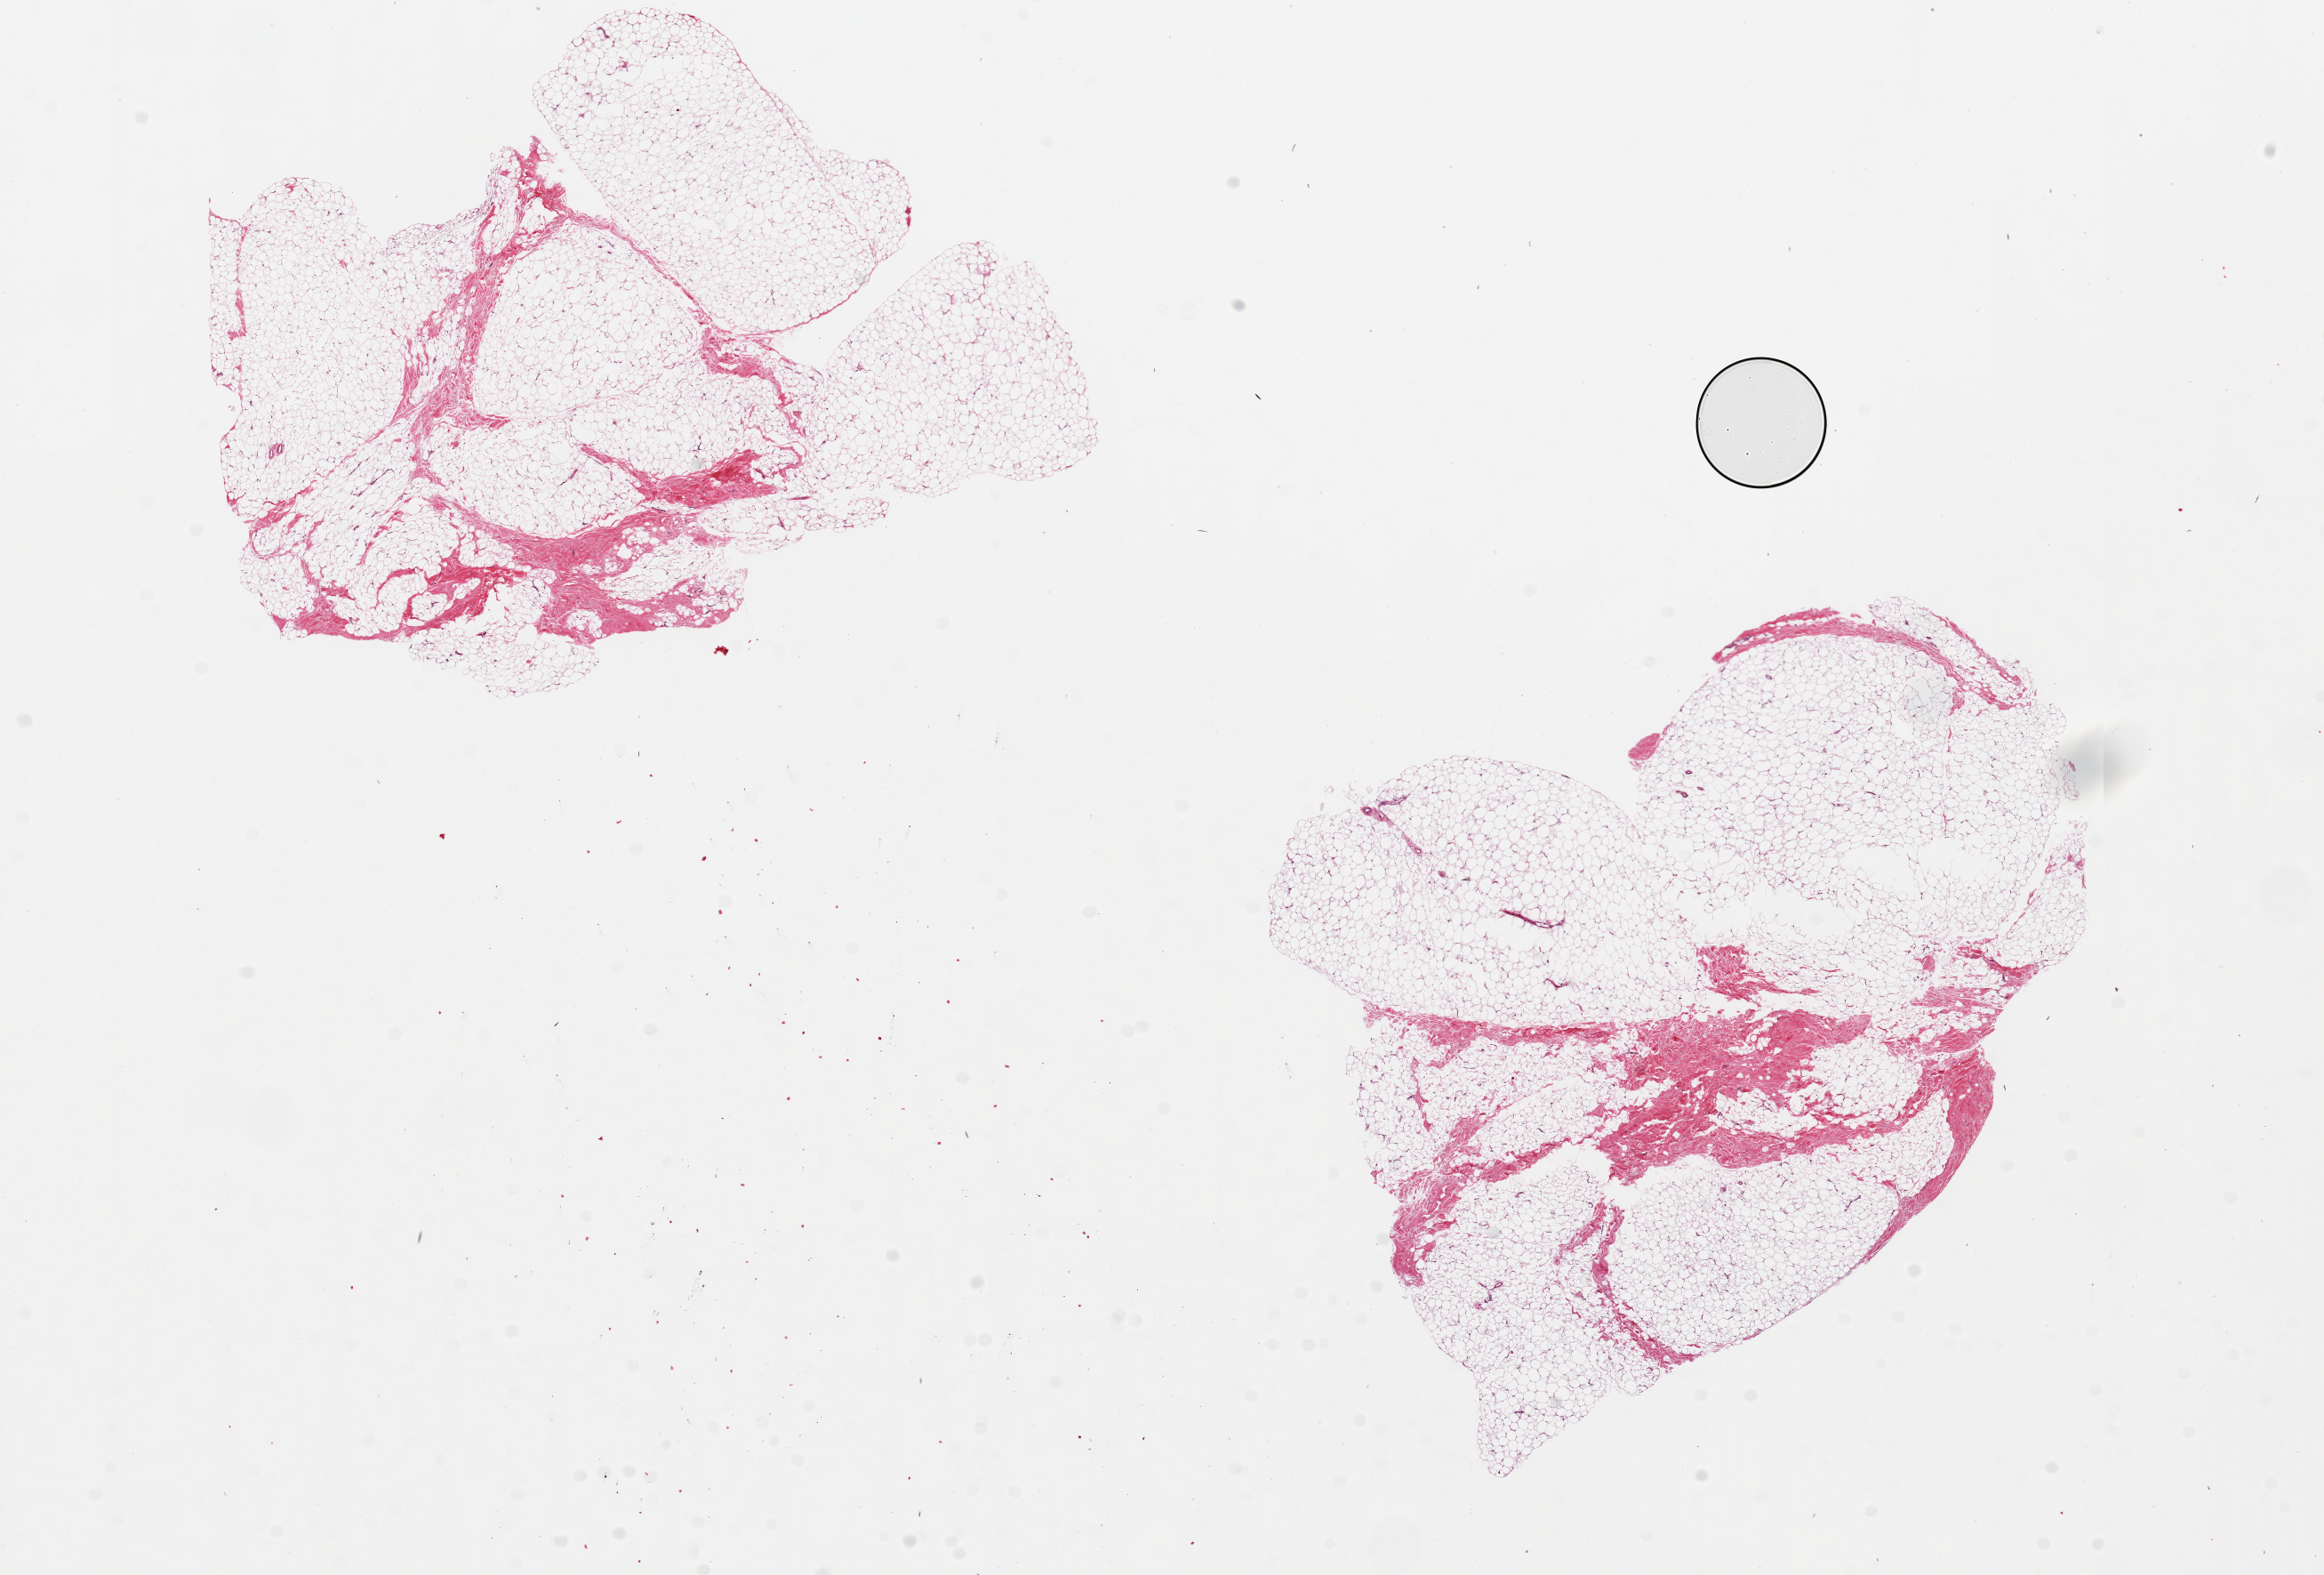
H&E whole-slide image, whole scanned area (about 20.7 x 14.0 mm, slide scanned at 20x) shown as a low-resolution overview. PAXgene-fixed, paraffin-embedded tissue. Section of breast (target tissue). Donor tissue sample. Donor: male.
Review note (as recorded): 2 pieces, 7x6.5 & 8x6mm; No mammary tissue, only fibroadipose.